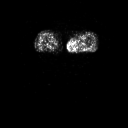
FDG PET of an extremity soft-tissue mass (from a PET/CT study), one axial slice. Position 2 of 91 along the scan axis. 3.27 mm slice thickness. 128 × 128 image matrix. Female patient, age 74 years. From the clinical record (not read from this slice): histological type: pleomorphic leiomyosarcoma; grade: high; site of the primary tumour: left thigh.
Annotated regions visible in this slice (expert contour drawn on MRI and transferred to this co-registered scan by the dataset authors):
- gross tumour volume including surrounding oedema: bounding box <73,36,86,49> (left, top, right, bottom; pixels)